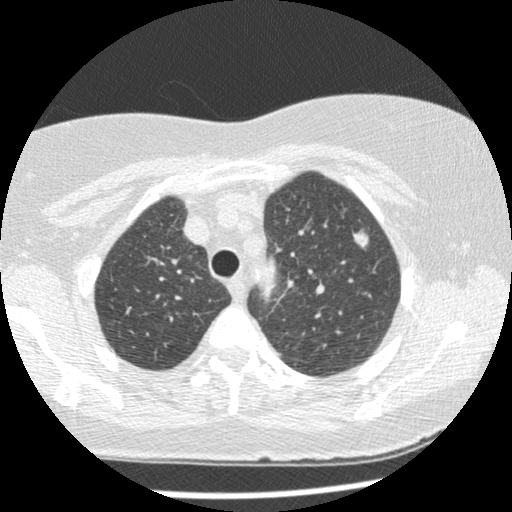
Low-dose screening chest CT, one axial slice. Position 185 of 241 along the scan axis. 120 kVp. Lung window (W 1500 / L -600 HU). 1.25 mm slice thickness. 512 × 512 image matrix, field of view 305 × 305 mm.
Outlined on this slice (outlined manually by an expert reader):
- lesion 2 (tumor, upper lobe of left lung): box from (x=352, y=229) to (x=369, y=250) px